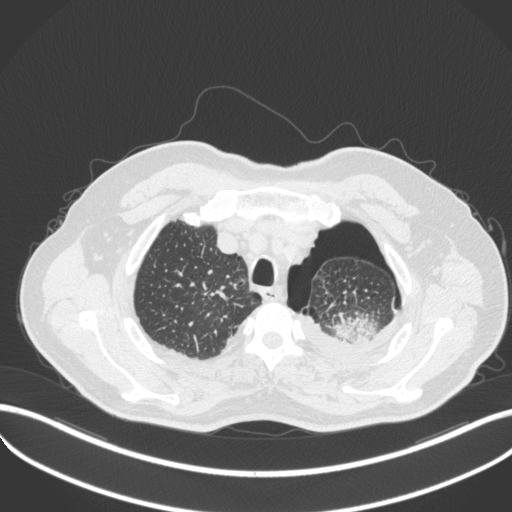
Chest CT, one axial slice. Reconstruction kernel B31f. Lung window (W 1500 / L -600 HU). 1 mm slice thickness. 512 × 512 image matrix, field of view 400 × 400 mm. Patient: male, 76 years. From the clinical record (not read from this slice): clinical TNM (as recorded): T3 N0 M1b.
Outlined on this slice (bounding box drawn by a radiologist):
- lung tumour (recorded histology: adenocarcinoma): bounding box (x1, y1, x2, y2) in pixels: (327, 309, 381, 346)